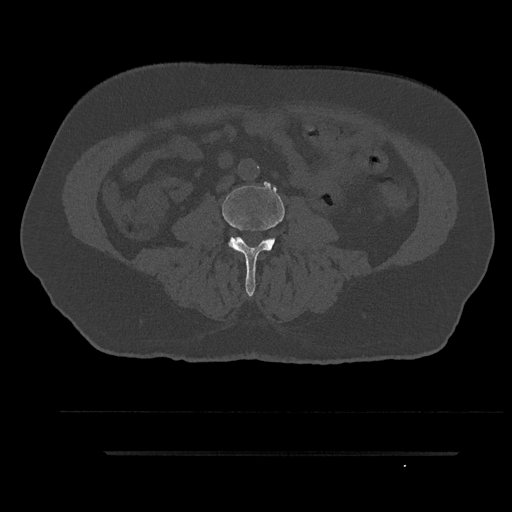
CT including the spine, one axial slice. Position 29 of 797 along the scan axis. Bone window (W 1800 / L 400 HU). 512 × 512 image matrix, field of view 432 × 432 mm. Male patient, age 63 years. Case-level facts recorded for this patient, not image findings: primary cancer: renal.
Outlined on this slice (semi-automatically segmented with operator editing):
- L3 vertebra: bounding box [x1, y1, x2, y2] px = [222, 185, 285, 297]